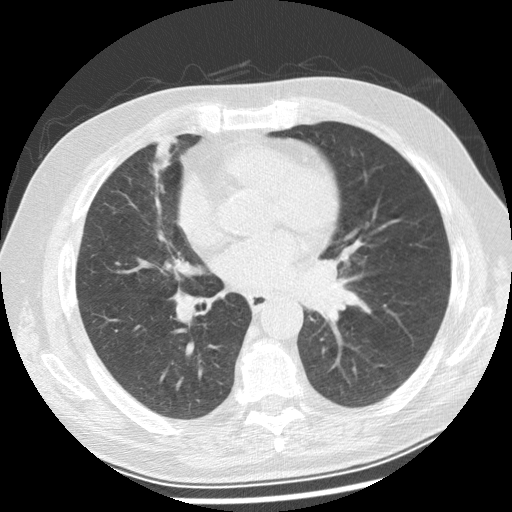
Low-dose screening chest CT, axial slice, baseline screening round, lung window (W 1500 / L -600 HU), 2.5 mm slice thickness, standard (soft-tissue) reconstruction kernel (STANDARD), 120 kVp, 512 × 512 image matrix. Male, age 70 years at enrolment.
- Expert reader's lesion annotation, bounding box (x1, y1, x2, y2) in pixels: (293, 240, 378, 326).
- Screening reader's record for this exam: no non-calcified nodule ≥4 mm recorded.
- Later outcome: lung cancer diagnosed 29 days after this screen — squamous cell carcinoma, keratinizing, NOS, left main stem bronchus, moderately differentiated (G2), stage IIIB (AJCC 6th edition), 40 mm at pathology.